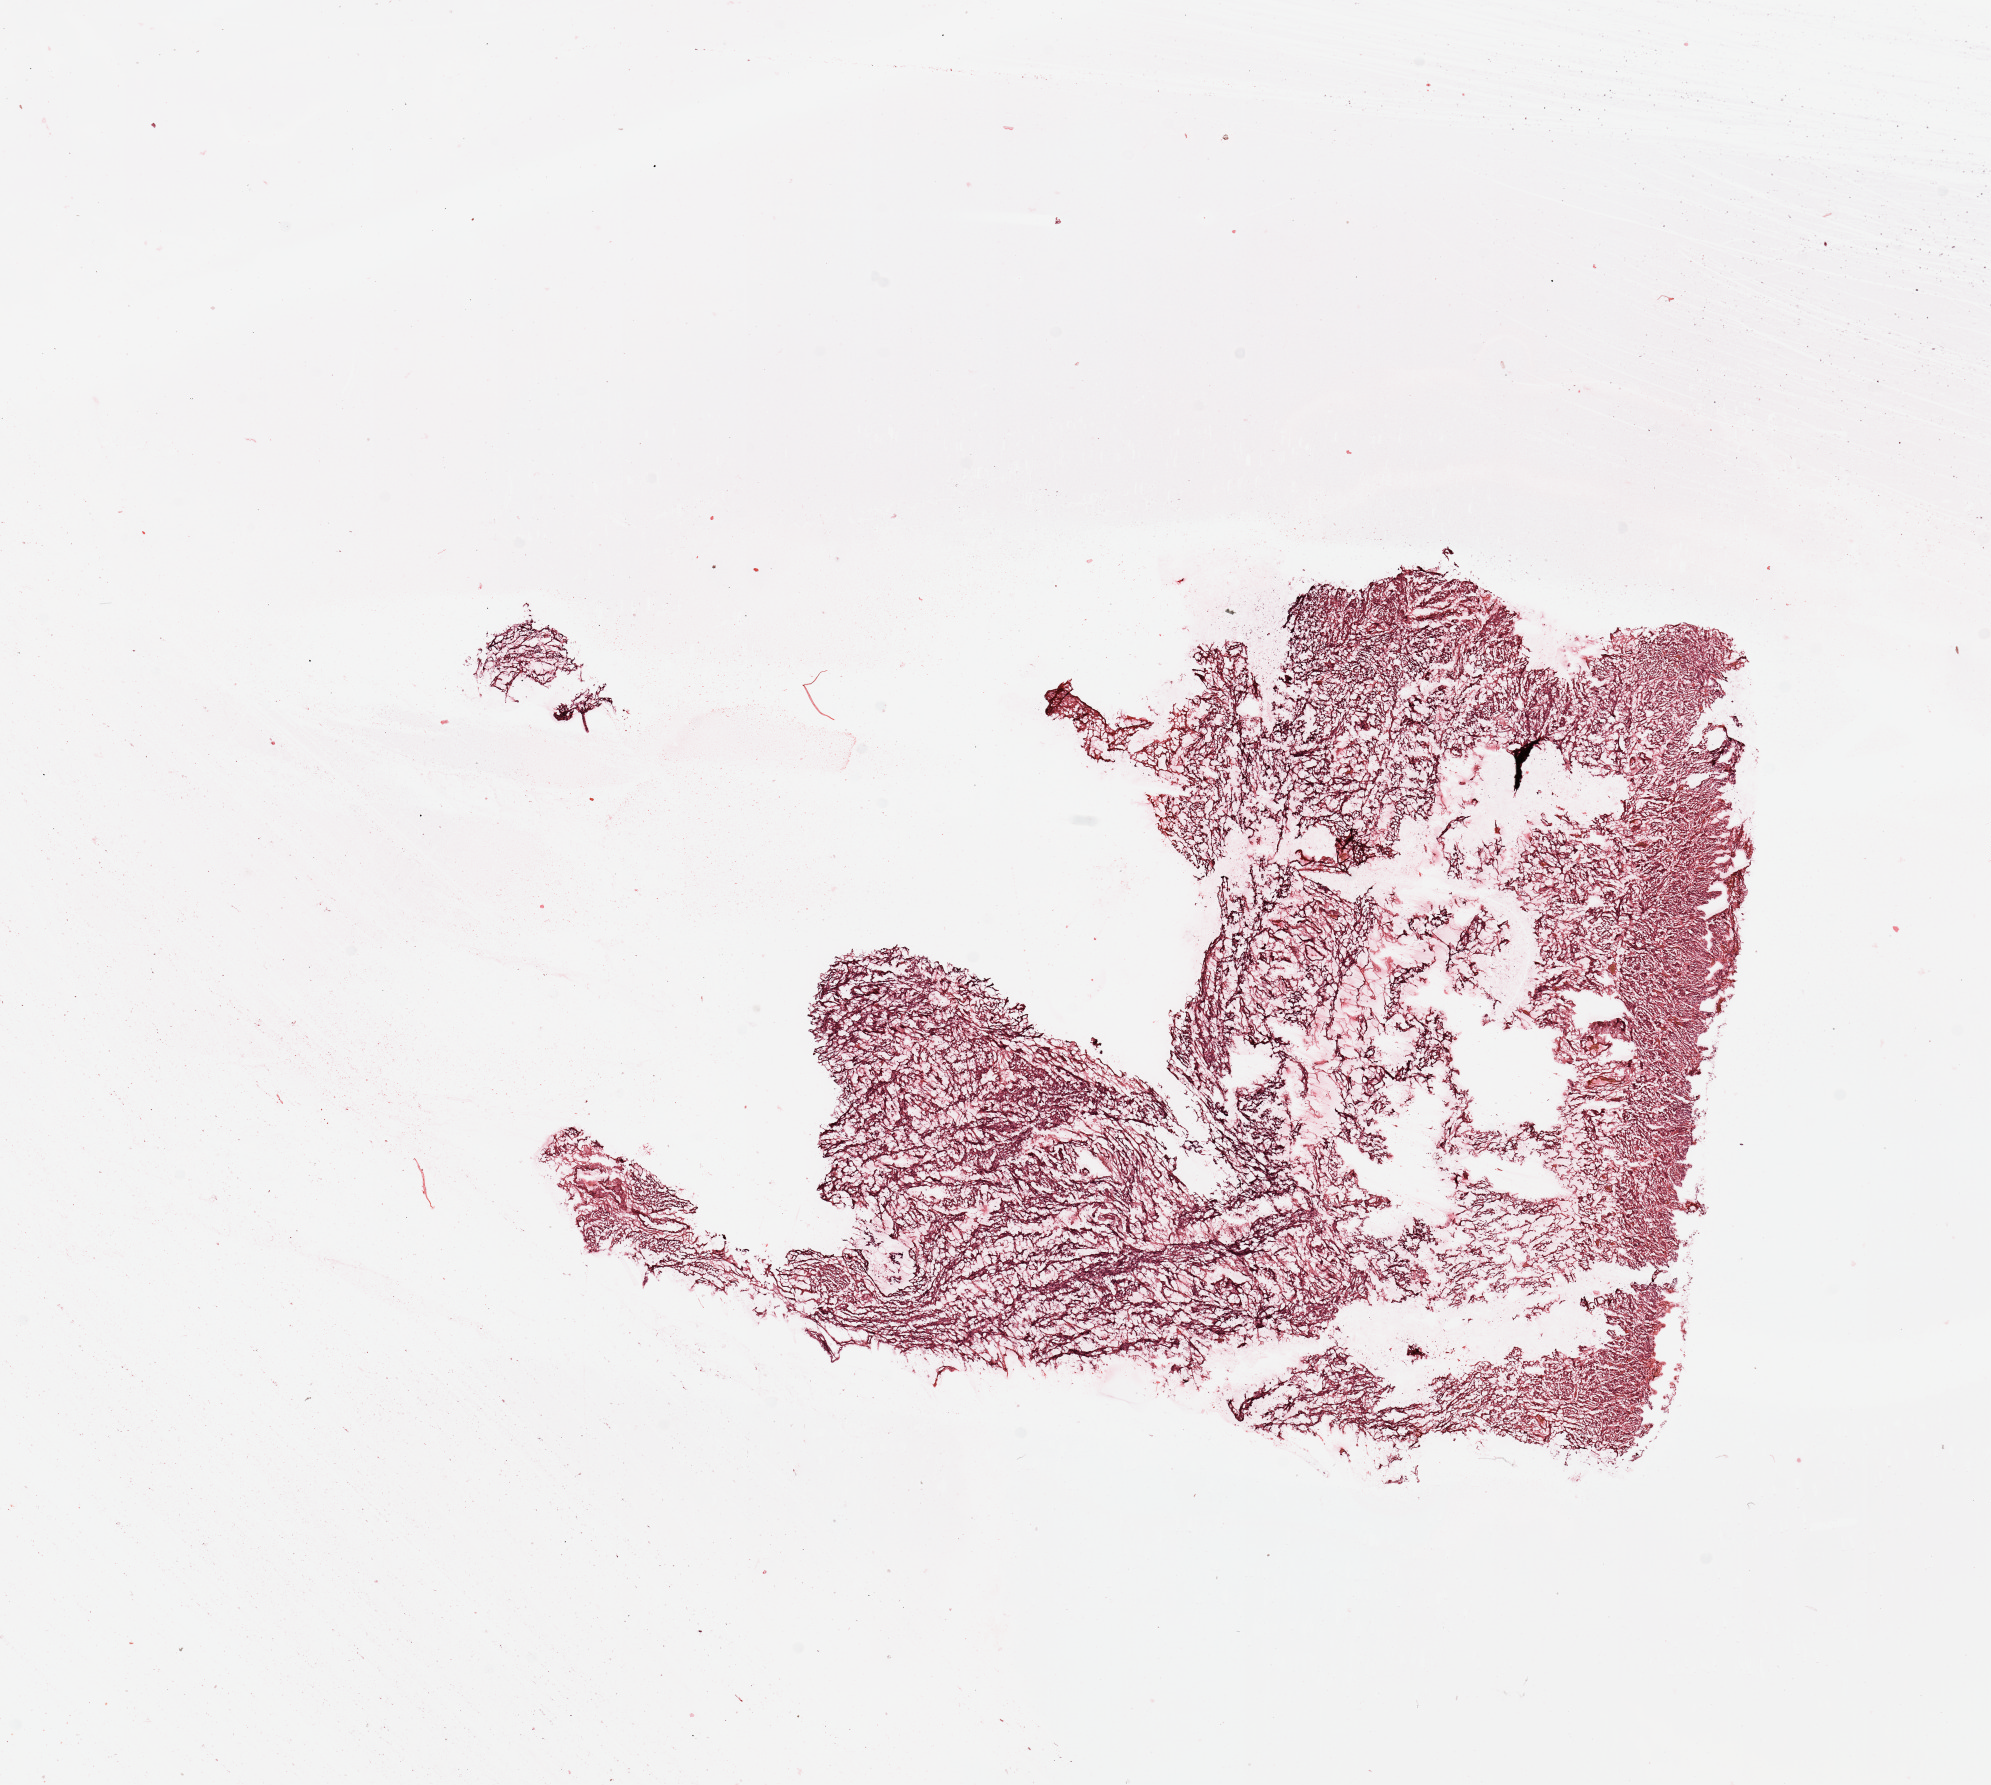
H&E-stained whole-slide image — low-resolution overview of the scanned area, about 15.8 x 14.1 mm. Uterus, normal (non-tumour) tissue. Patient: female, age 67 years.
This section: normal (non-tumour) tissue from the same patient. Patient diagnosis: Endometrioid adenocarcinoma, NOS.